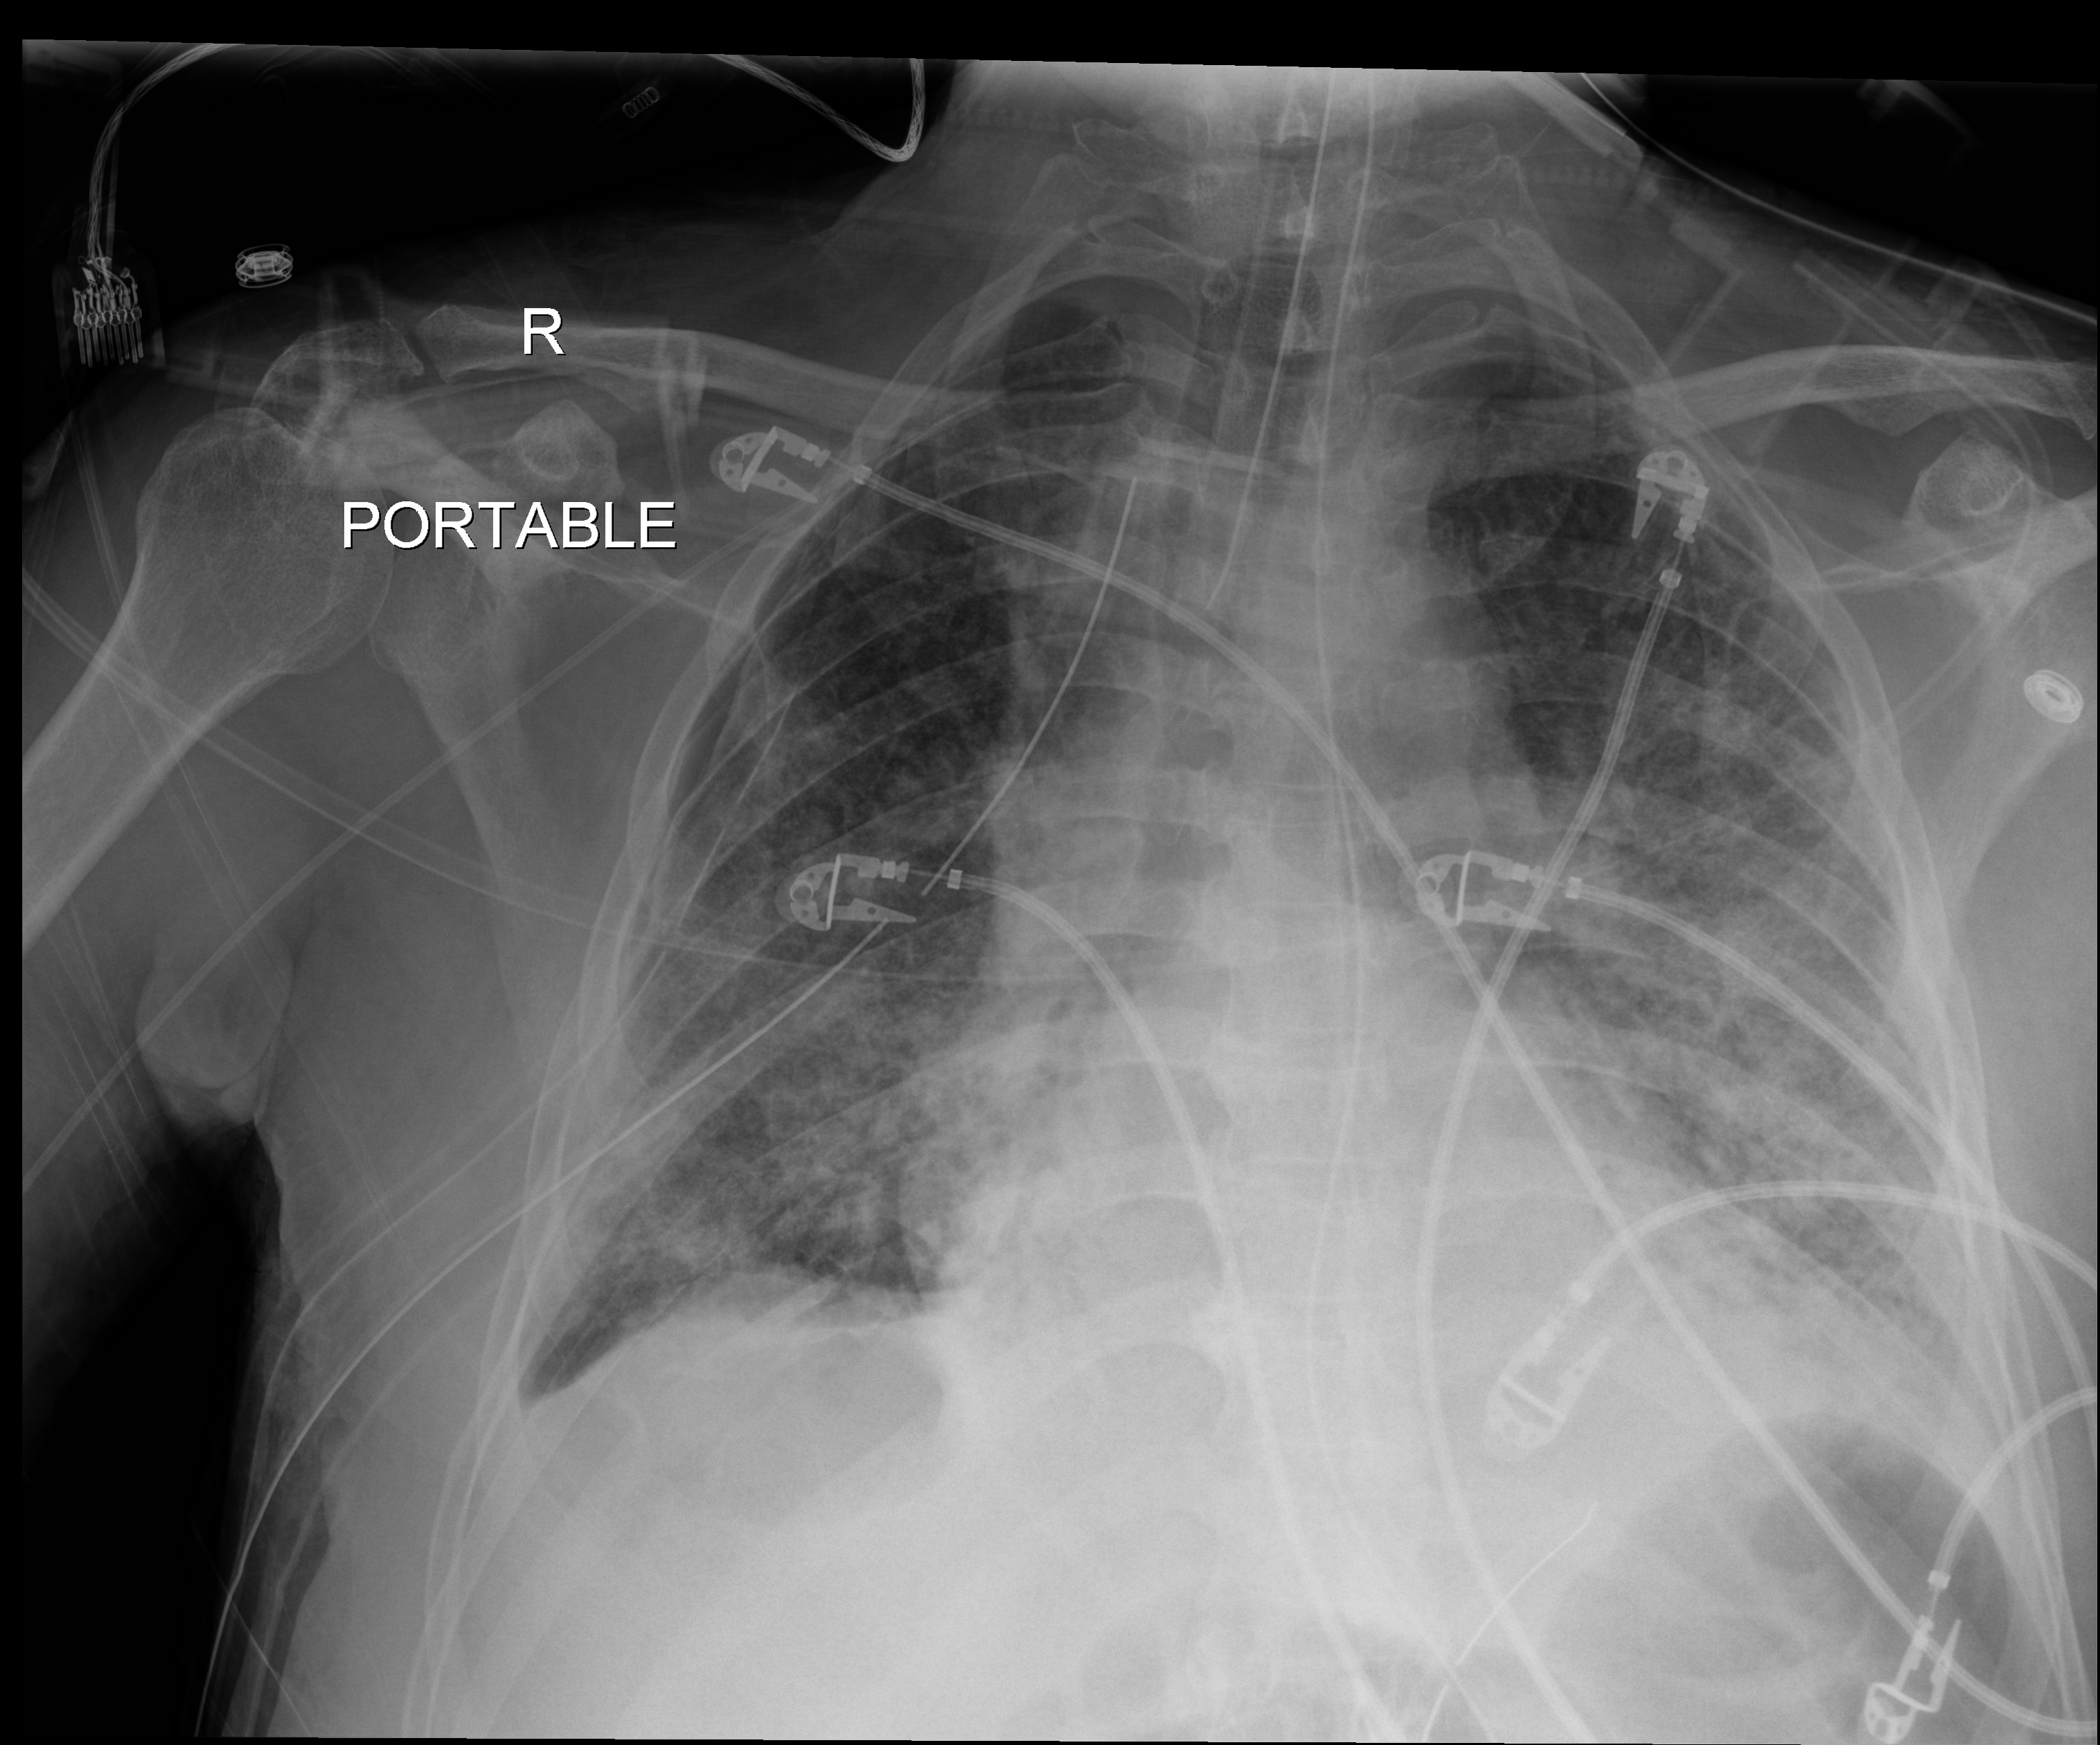
Chest X-ray (portable). Patient hospitalised with COVID-19; male, aged 60–74 years.
Admission-level facts for this patient (not findings on this image; timing relative to this image not recorded):
- admitted to intensive care during this hospital stay: yes